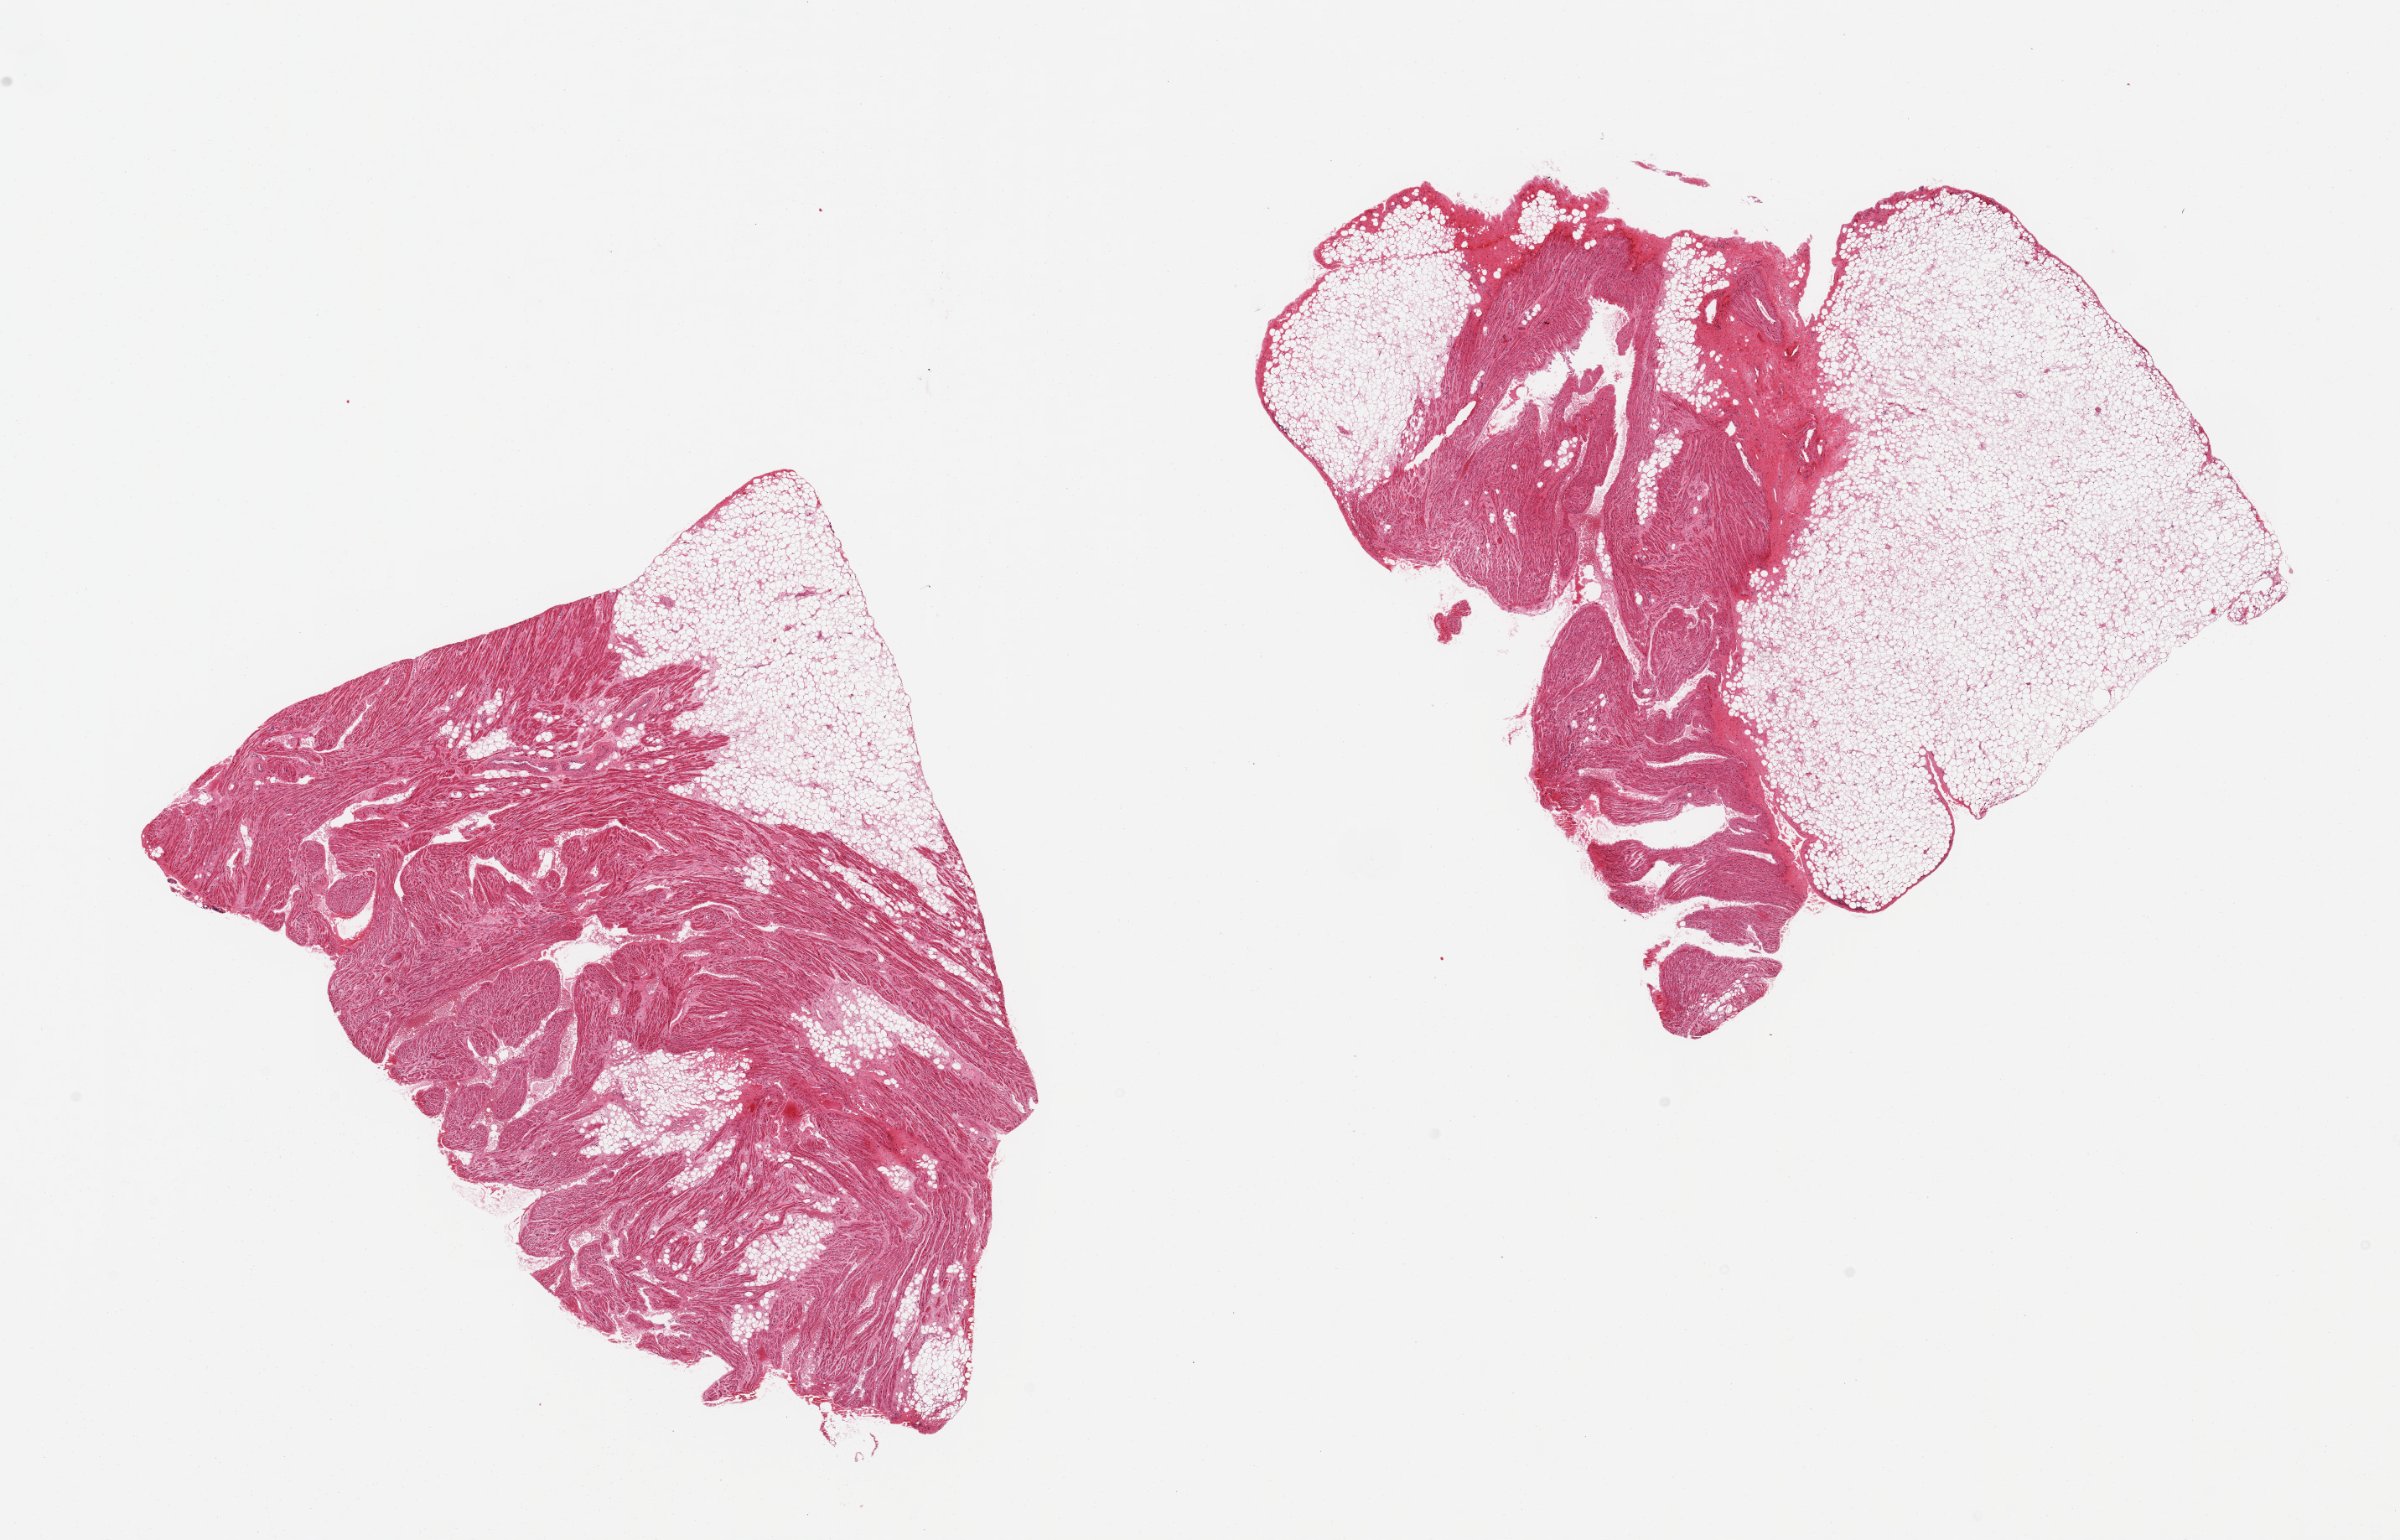
Digitized H&E-stained section — shown as a low-resolution overview of the whole scanned area (about 22.6 x 14.5 mm); PAXgene-fixed, paraffin-embedded tissue; target tissue: auricular appendage; tissue donor sample.
Reviewer comment on this tissue sample: 2 pieces, adherent/interstitial fat is ~40% of specimens.